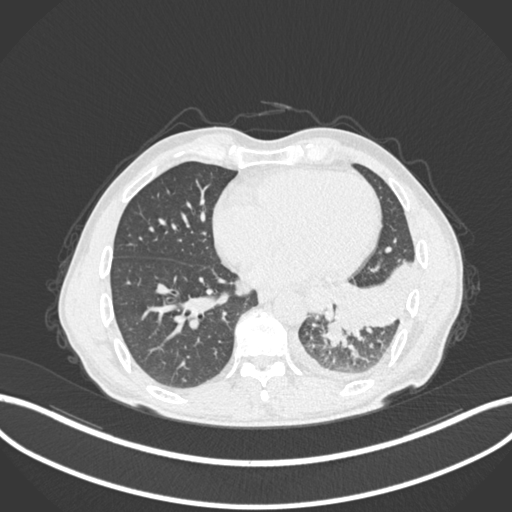
Chest CT, one axial slice. Position 88 of 222 along the scan axis. 120 kVp. Lung window (W 1500 / L -600 HU). 1 mm slice thickness. 512 × 512 image matrix. Male patient, age 47 years. Case-level facts recorded for this patient, not image findings: clinical TNM (as recorded): T3 N1 M1c; histopathological grade: G3.
Outlined on this slice (rectangle marked by the reading radiologist):
- lung tumour (recorded histology: small cell carcinoma): bounding box [x1, y1, x2, y2] px = [321, 318, 348, 350]